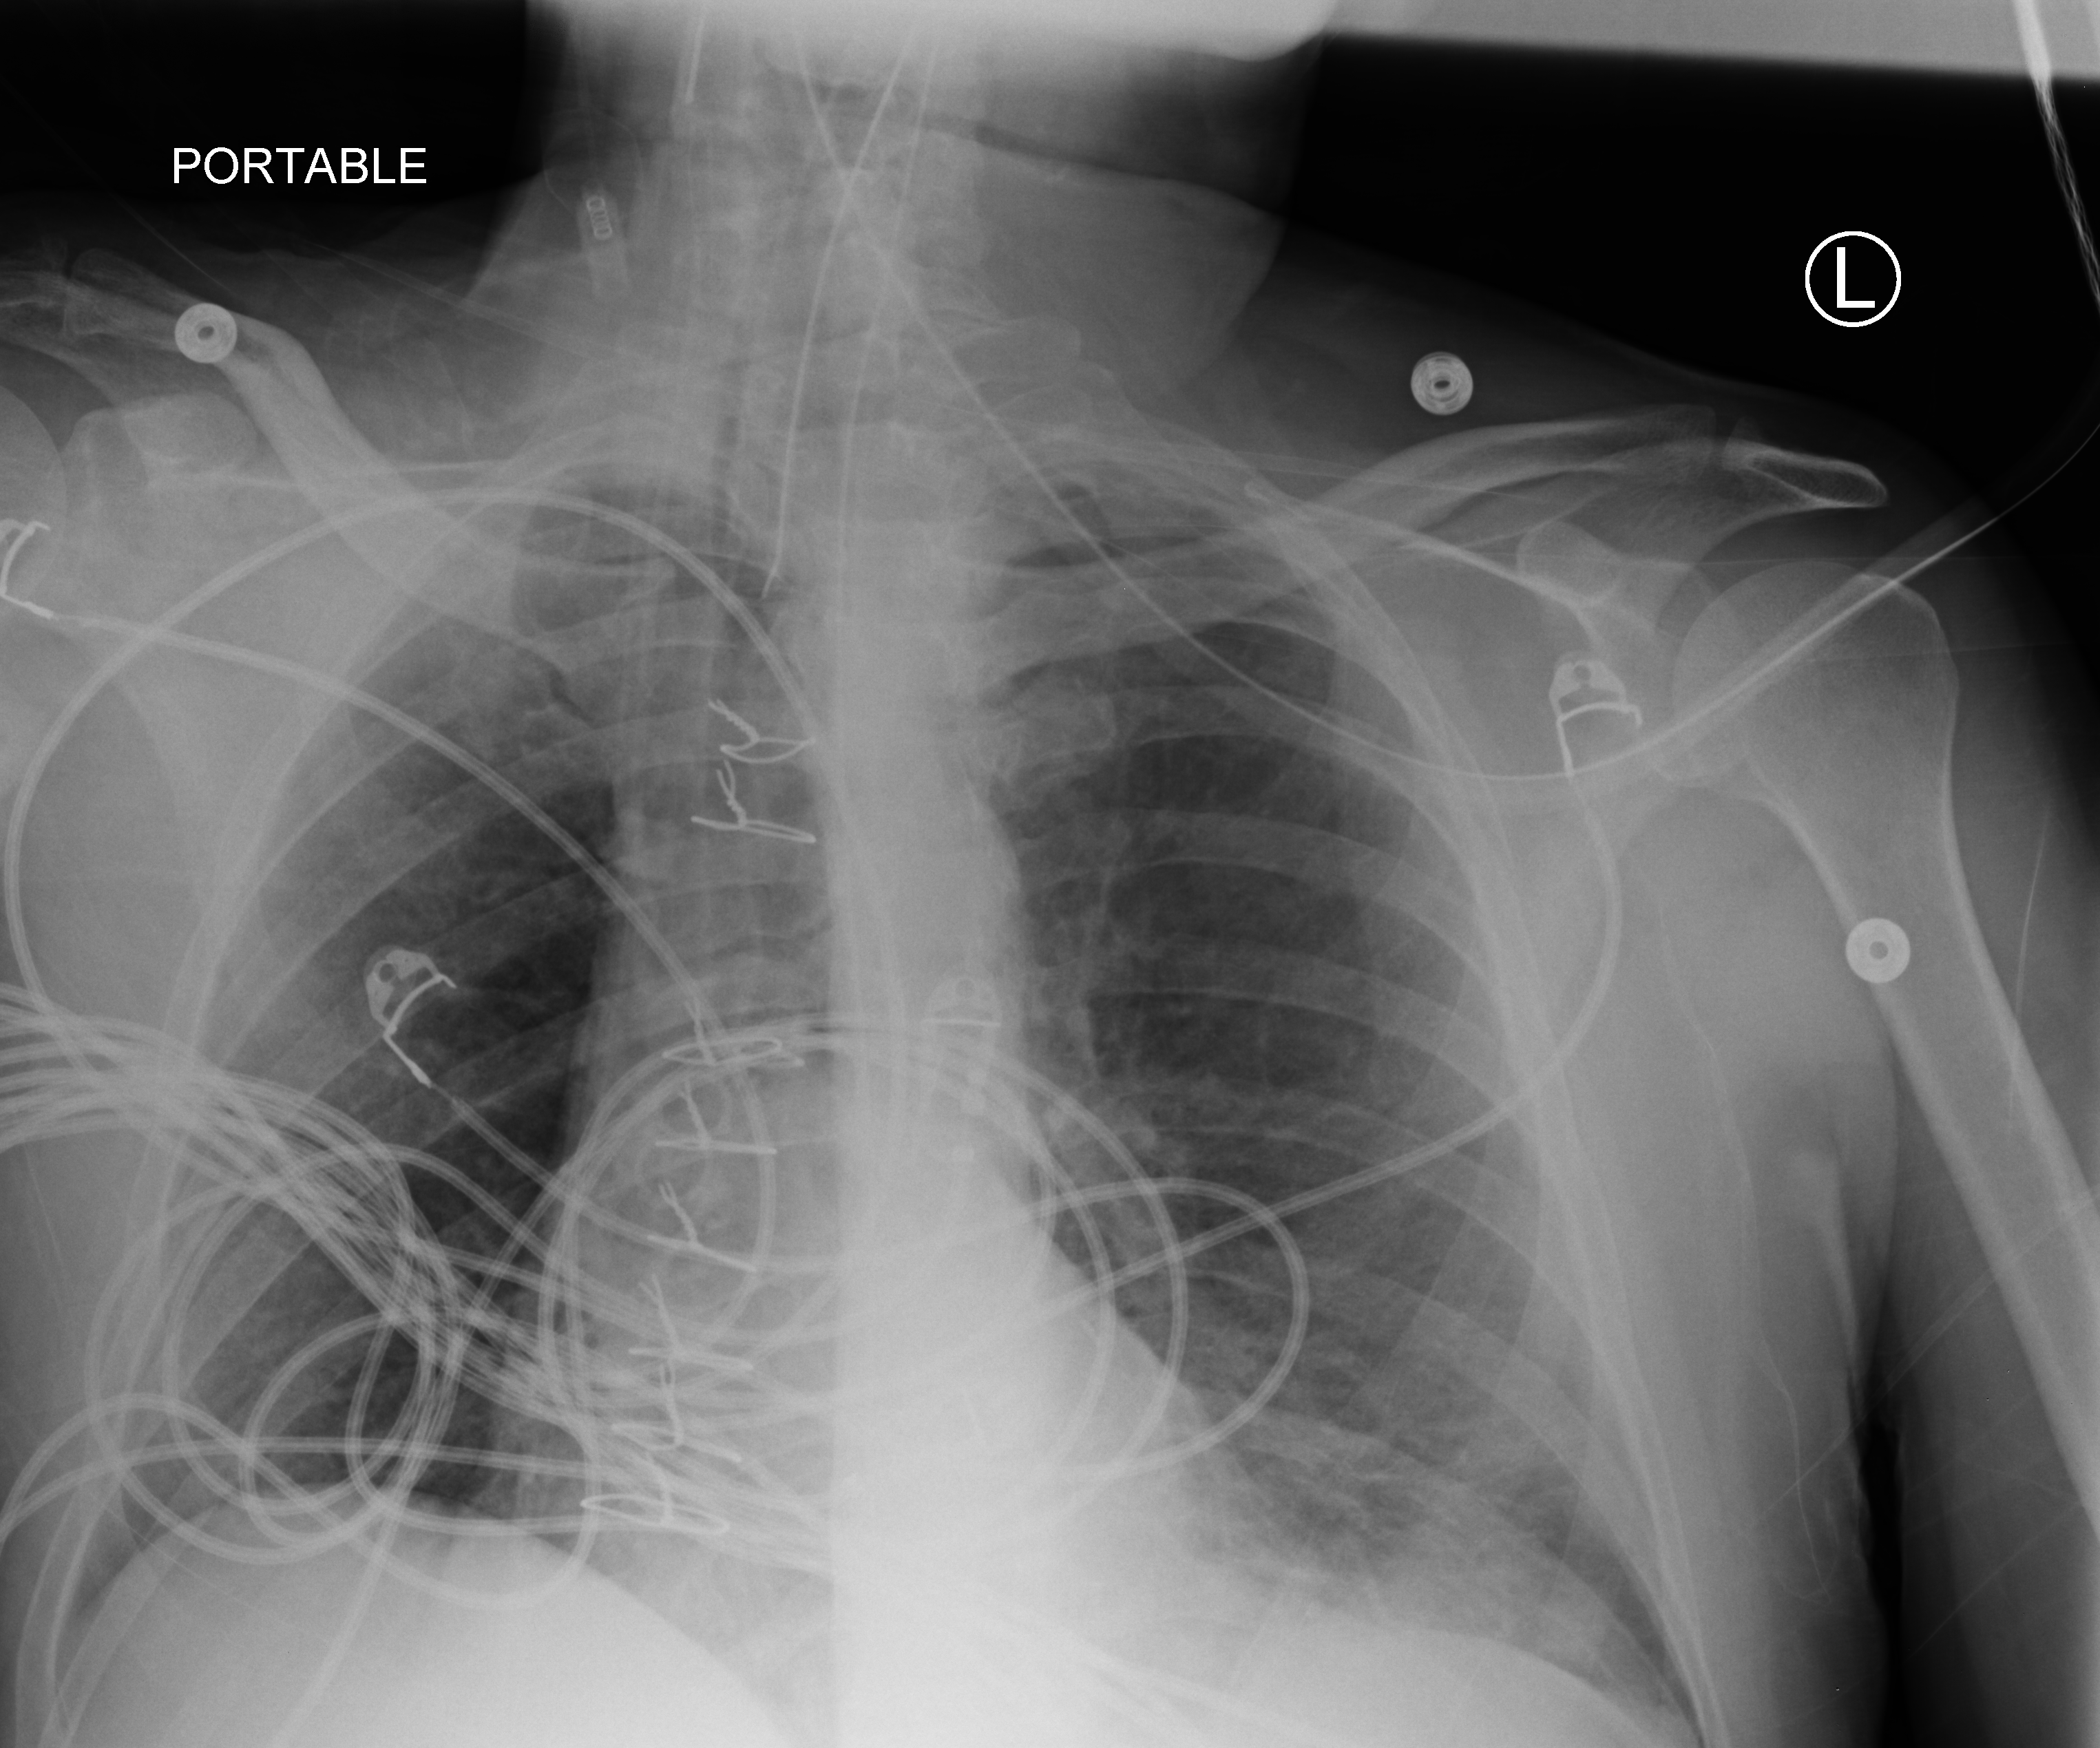
Portable chest radiograph, anteroposterior (AP) projection. Patient hospitalised with COVID-19; male, aged 18–59 years.
From the hospital-stay record, not from the radiograph (when in the stay this image was taken is not recorded):
- length of hospital stay: 63 days